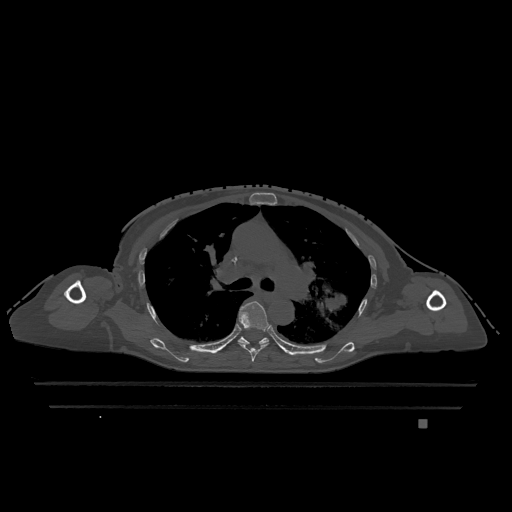
CT including the spine, one axial slice. Position 817 of 1317 along the scan axis. Bone window (W 1800 / L 400 HU). 0.5 mm slice thickness. 512 × 512 image matrix. Patient: female, 74 years. Case-level facts recorded for this patient, not image findings: primary cancer: lung; vertebrae with lytic lesions (as recorded): T1, T4, T5, T6, L4, L5.
Annotated regions visible in this slice (semi-automatically segmented with operator editing):
- T5 vertebra: bounding box <238,301,269,362> (left, top, right, bottom; pixels)
- T6 vertebra: <238,337,269,344>